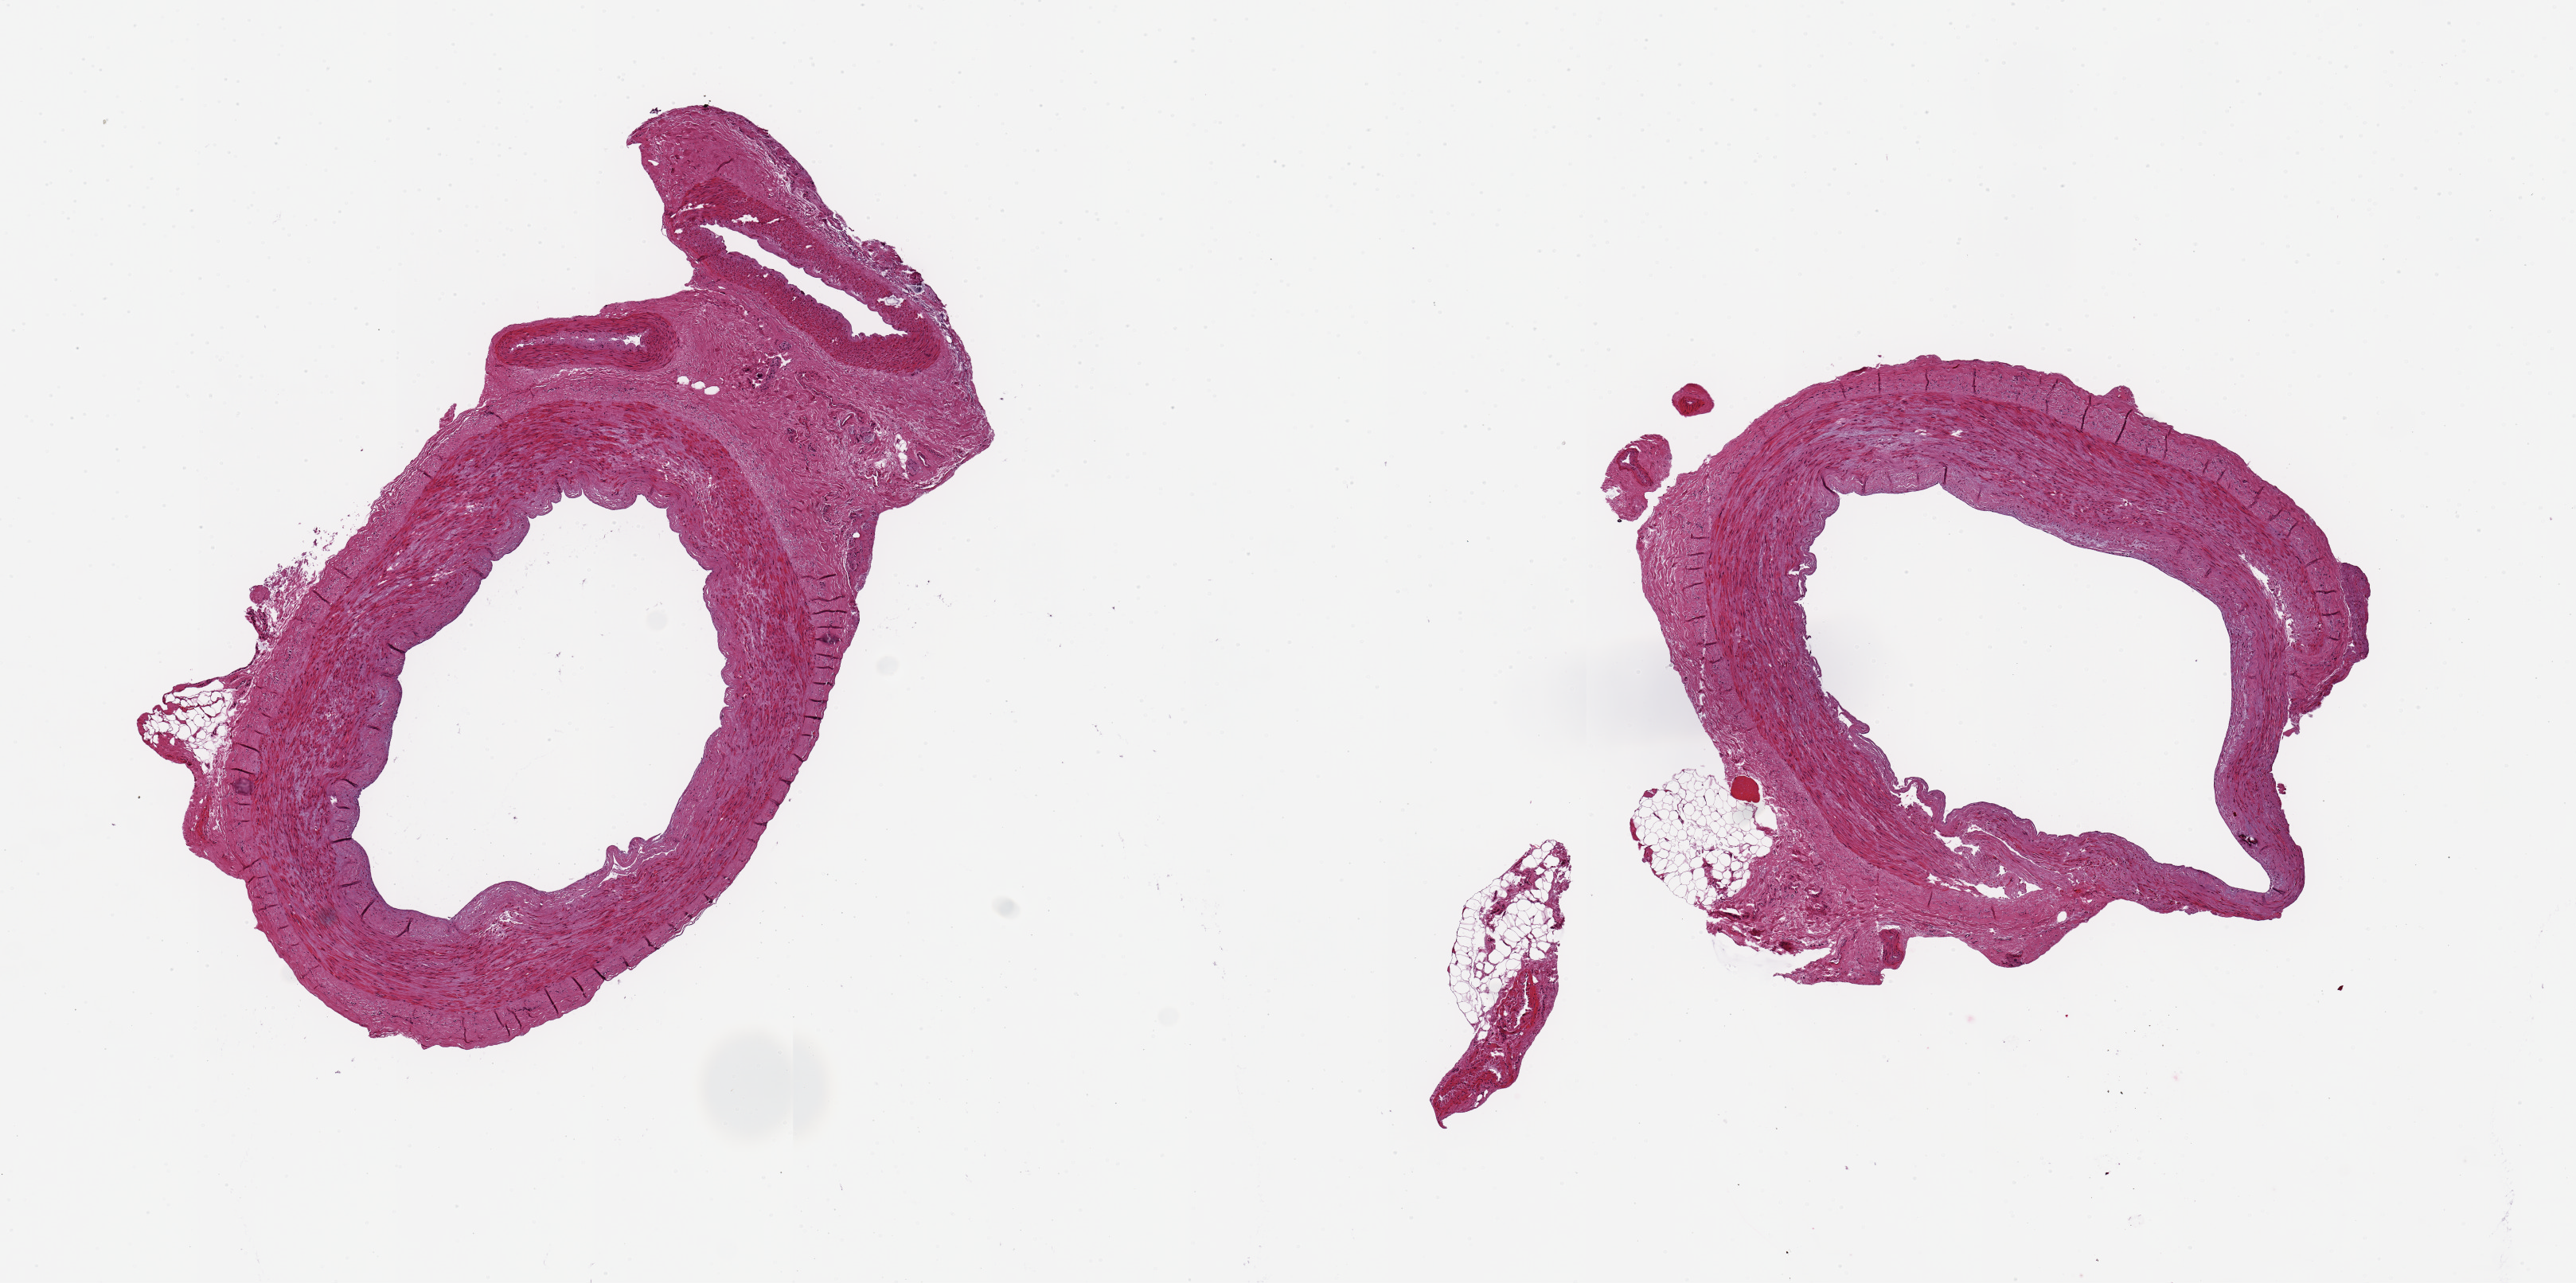
Whole-slide image, H&E stain — low-resolution overview of the scanned area, about 12.8 x 6.4 mm; PAXgene-fixed paraffin-embedded (PFPE) section; sampled site (target tissue): tibial artery; tissue donor sample. Donor sex: female.
Reviewer comment on this tissue sample: 2 pieces, each ~2.5x3.5 mm; minimal adipose.